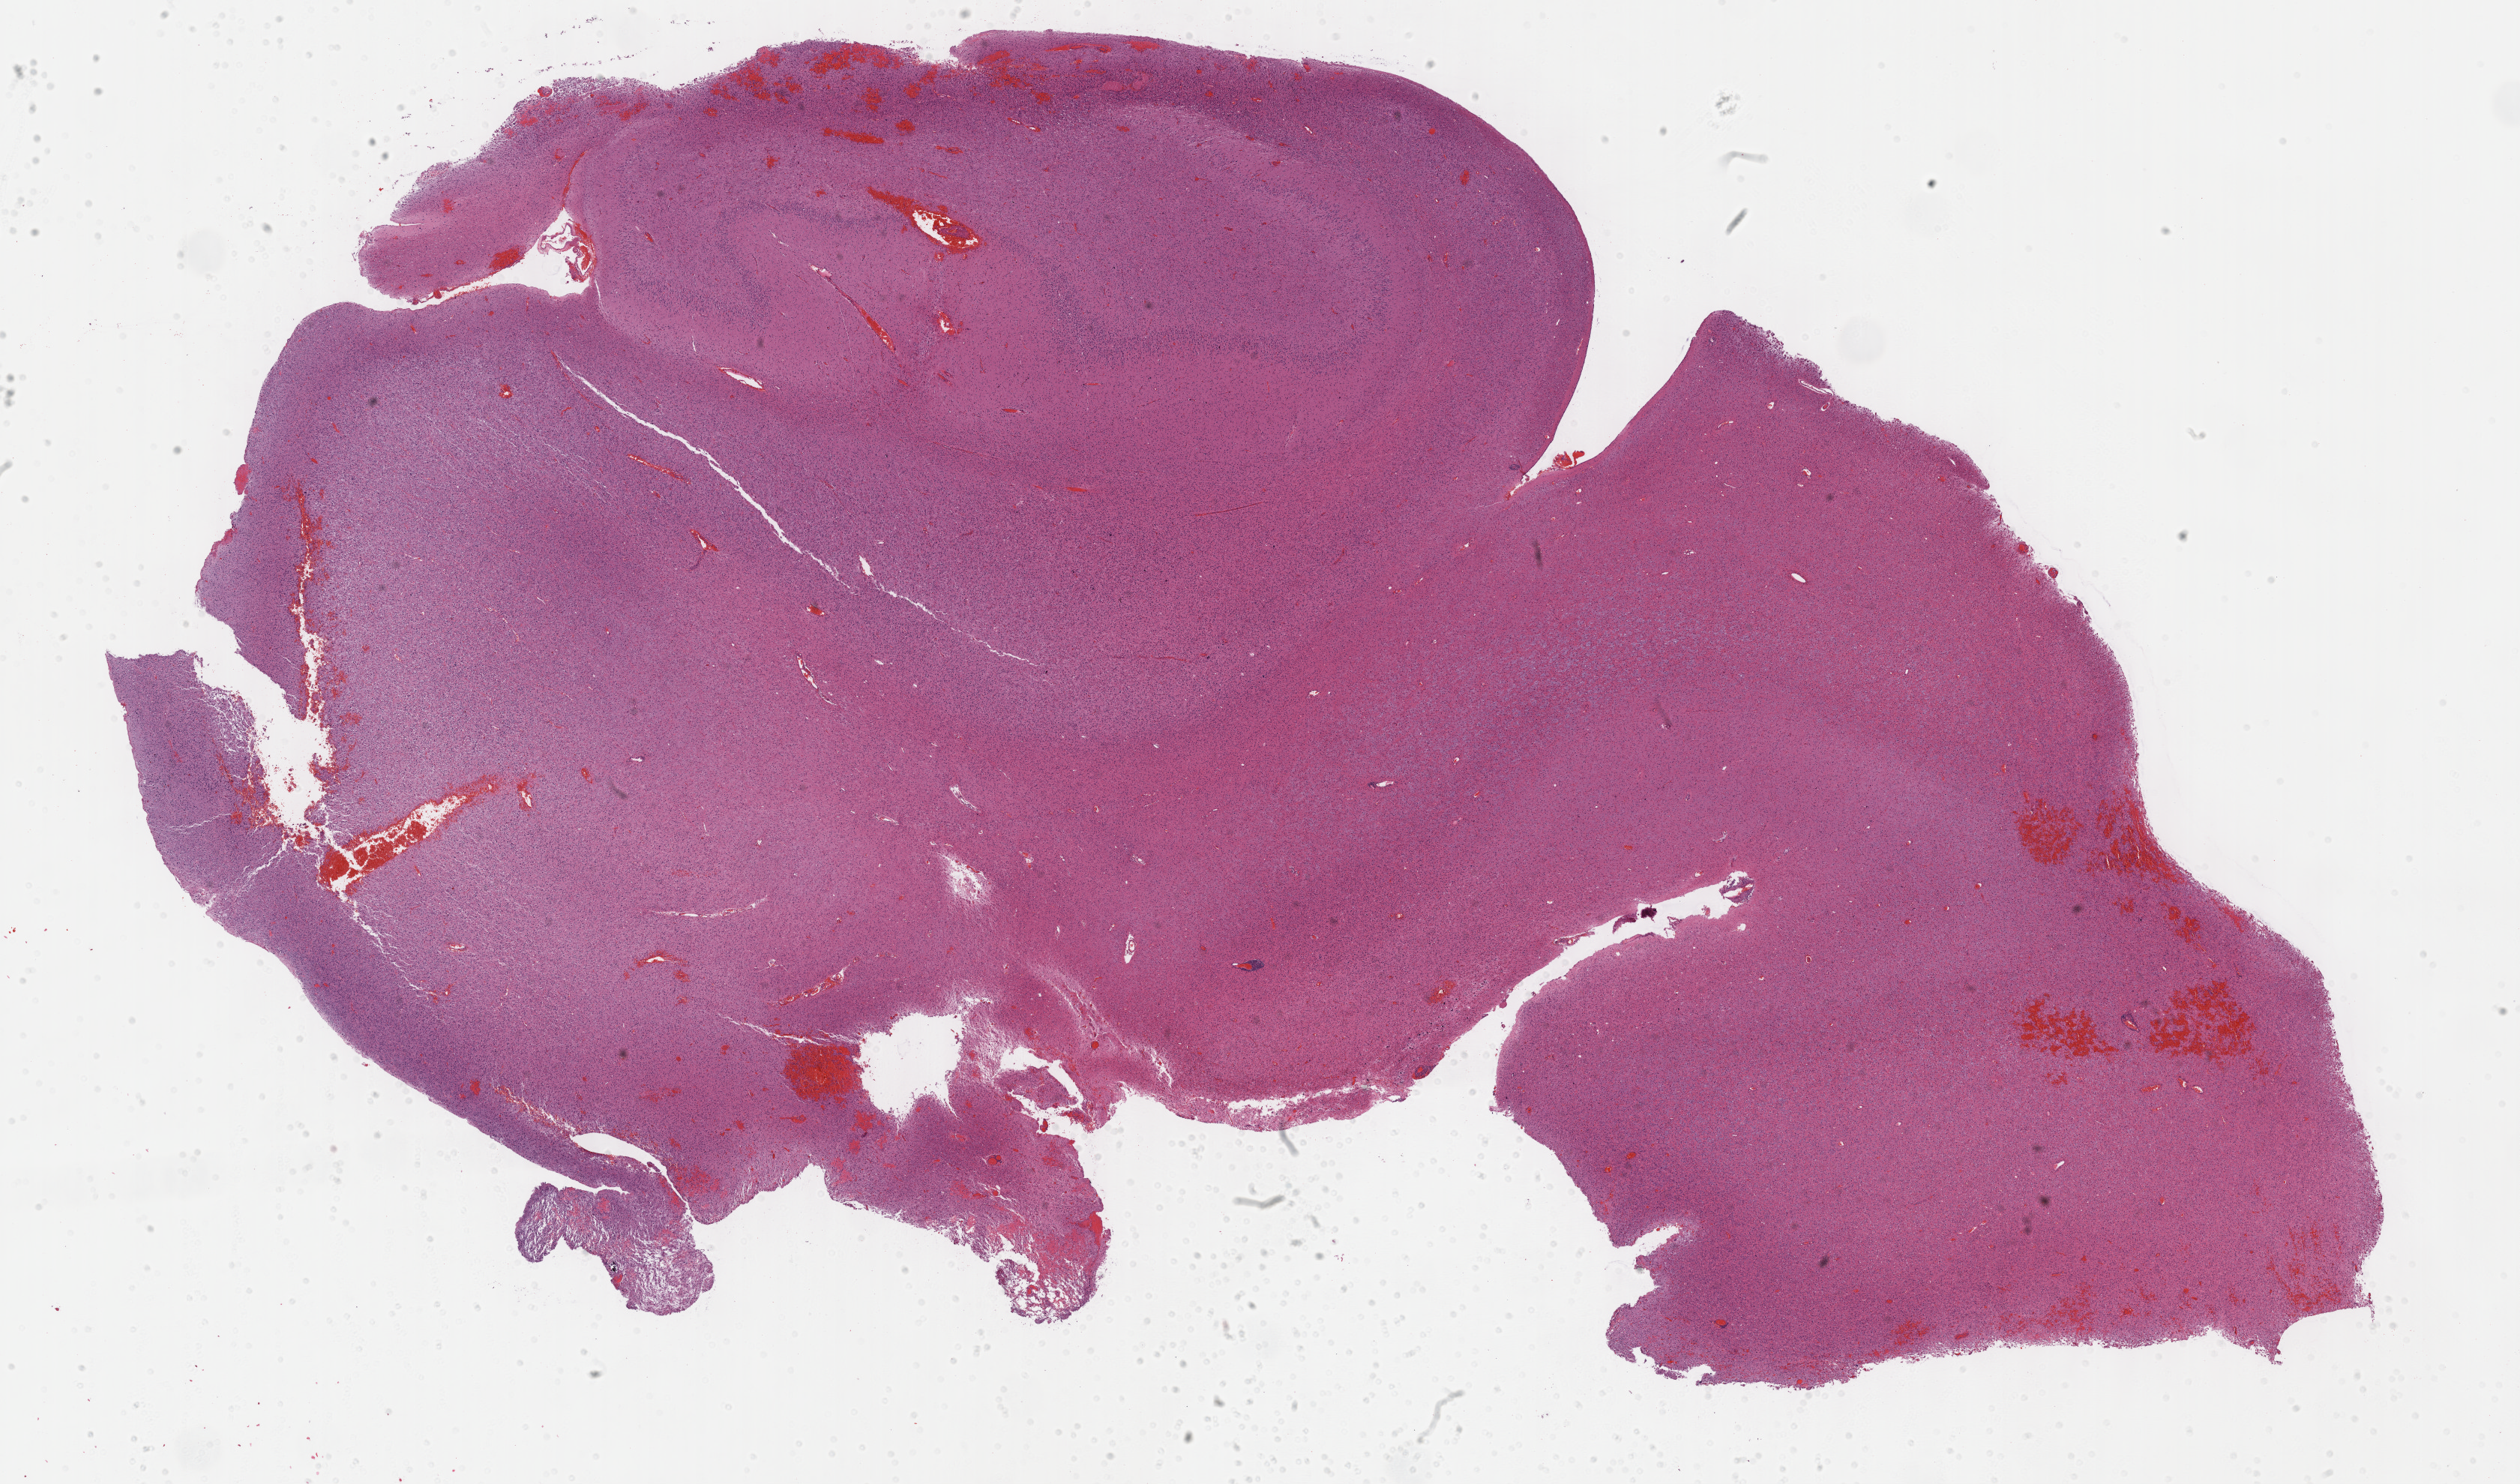
Whole-slide histology image, Hematoxylin and eosin (H&E) stained, shown as a low-resolution overview of the whole scanned area (about 27.2 x 16.0 mm, slide scanned at 40x); formalin-fixed paraffin-embedded (FFPE) diagnostic section; brain, primary tumour sample. Male, age 37 years at initial diagnosis.
Pathologic diagnosis: Oligodendroglioma, anaplastic.